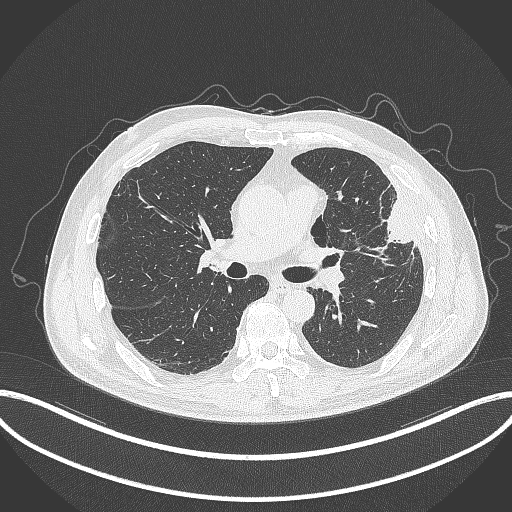
Chest CT, one axial slice; position 192 of 382 along the scan axis; reconstruction kernel B70f; 120 kVp; lung window (W 1500 / L -600 HU); 1 mm slice thickness; 512 × 512 image matrix. Male patient, age 64 years. From the clinical record (not read from this slice): clinical TNM (as recorded): T4 N1 M0.
Outlined on this slice (rectangle marked by the reading radiologist):
- lung tumour (recorded histology: adenocarcinoma): bounding box (x1, y1, x2, y2) in pixels: (374, 190, 414, 253)